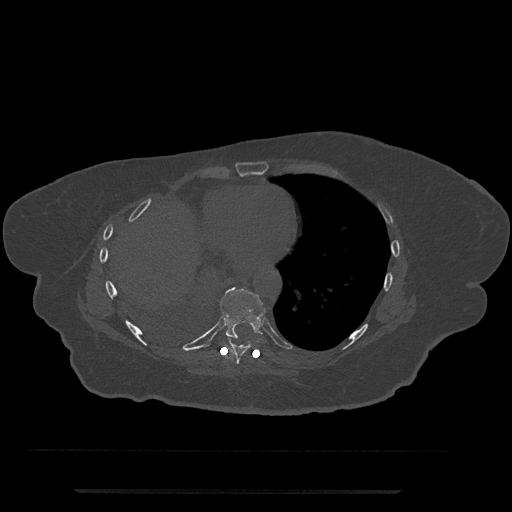
CT including the spine, one axial slice; position 364 of 797 along the scan axis; 120 kVp; bone window (W 1800 / L 400 HU); 0.5 mm slice thickness; 512 × 512 image matrix, field of view 440 × 440 mm. Patient: female, 51 years. From the clinical record (not read from this slice): primary cancer: neuro; vertebrae with lytic lesions (as recorded): T8.
Outlined on this slice (semi-automatically segmented with operator editing):
- T8 vertebra: bounding box (x1, y1, x2, y2) in pixels: (228, 339, 249, 364)
- T9 vertebra: (220, 287, 266, 341)